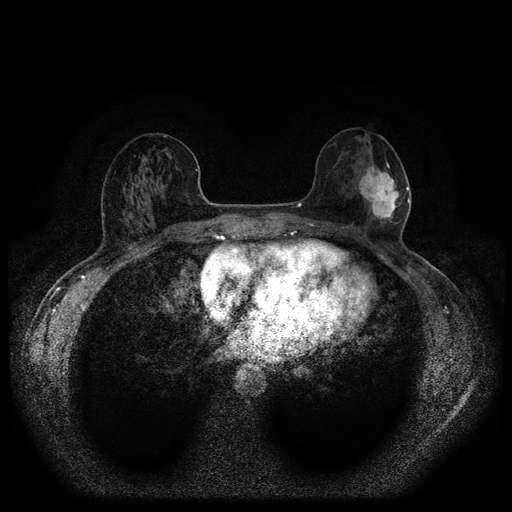
Breast MRI (dynamic contrast-enhanced, multi-phase), one axial slice; position 48 of 116 along the scan axis; dynamic contrast-enhanced series, time point 2 of 5 at this slice position (early post-contrast); 1.5 T; TE 2.7 ms, TR 5.4 ms; 2 mm slice thickness; 512 × 512 image matrix. Female patient, age 56 years.
Structures marked on this image (semi-automatically segmented with operator editing):
- breast lesion (labelled 'tumour' in the annotation; benign lesions carry a separate 'benign' label): bounding box (x1, y1, x2, y2) in pixels: (357, 164, 401, 225)